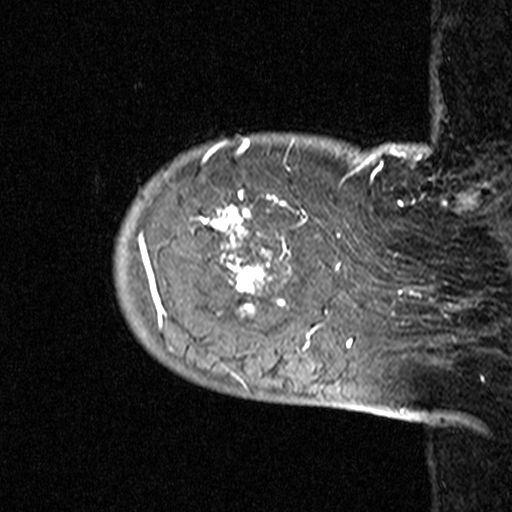
Breast MRI (dynamic contrast-enhanced), one sagittal slice; slice 6 of 44 in the series (ordered by position); dynamic contrast-enhanced study with each time point stored as its own series, time point 2 of 3 at this slice position (early post-contrast, ordered by acquisition time); 1.5 T; TE 4.5 ms, TR 11 ms; 3 mm slice thickness; 512 × 512 image matrix, field of view 200 × 200 mm. Patient: female, 53 years. Case-level facts recorded for this patient, not image findings: setting: breast cancer imaged before/during neoadjuvant chemotherapy; receptor status: HR-positive, HER2-negative.
Annotated regions visible in this slice (semi-automatically segmented with operator editing):
- analysis volume of interest (the breast-tissue region the enhancement analysis was run in; not a lesion): bounding box [x1, y1, x2, y2] px = [113, 140, 311, 353]
- tumour enhancement mask (voxels above the 90 % enhancement threshold inside the analysis volume of interest): [139, 140, 308, 326]